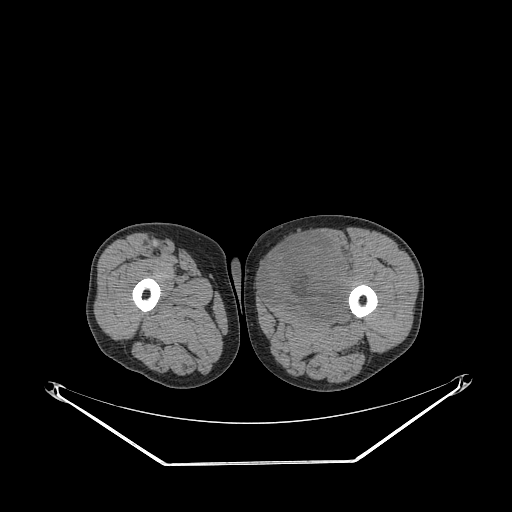
CT of an extremity soft-tissue mass (from a PET/CT study), one axial slice; slice 247 of 267 in the series (ordered by position); reconstruction kernel STANDARD; 140 kVp; soft-tissue window (W 400 / L 40 HU); 512 × 512 image matrix, field of view 500 × 500 mm. Male patient. From the clinical record (not read from this slice): histological type: pleiomorphic liposarcoma; grade: high; site of the primary tumour: left thigh.
Outlined on this slice (expert contour drawn on MRI and transferred to this co-registered scan by the dataset authors):
- gross tumour volume including surrounding oedema: bounding box [x1, y1, x2, y2] px = [263, 235, 355, 318]
- gross tumour volume (mass): [263, 235, 352, 318]